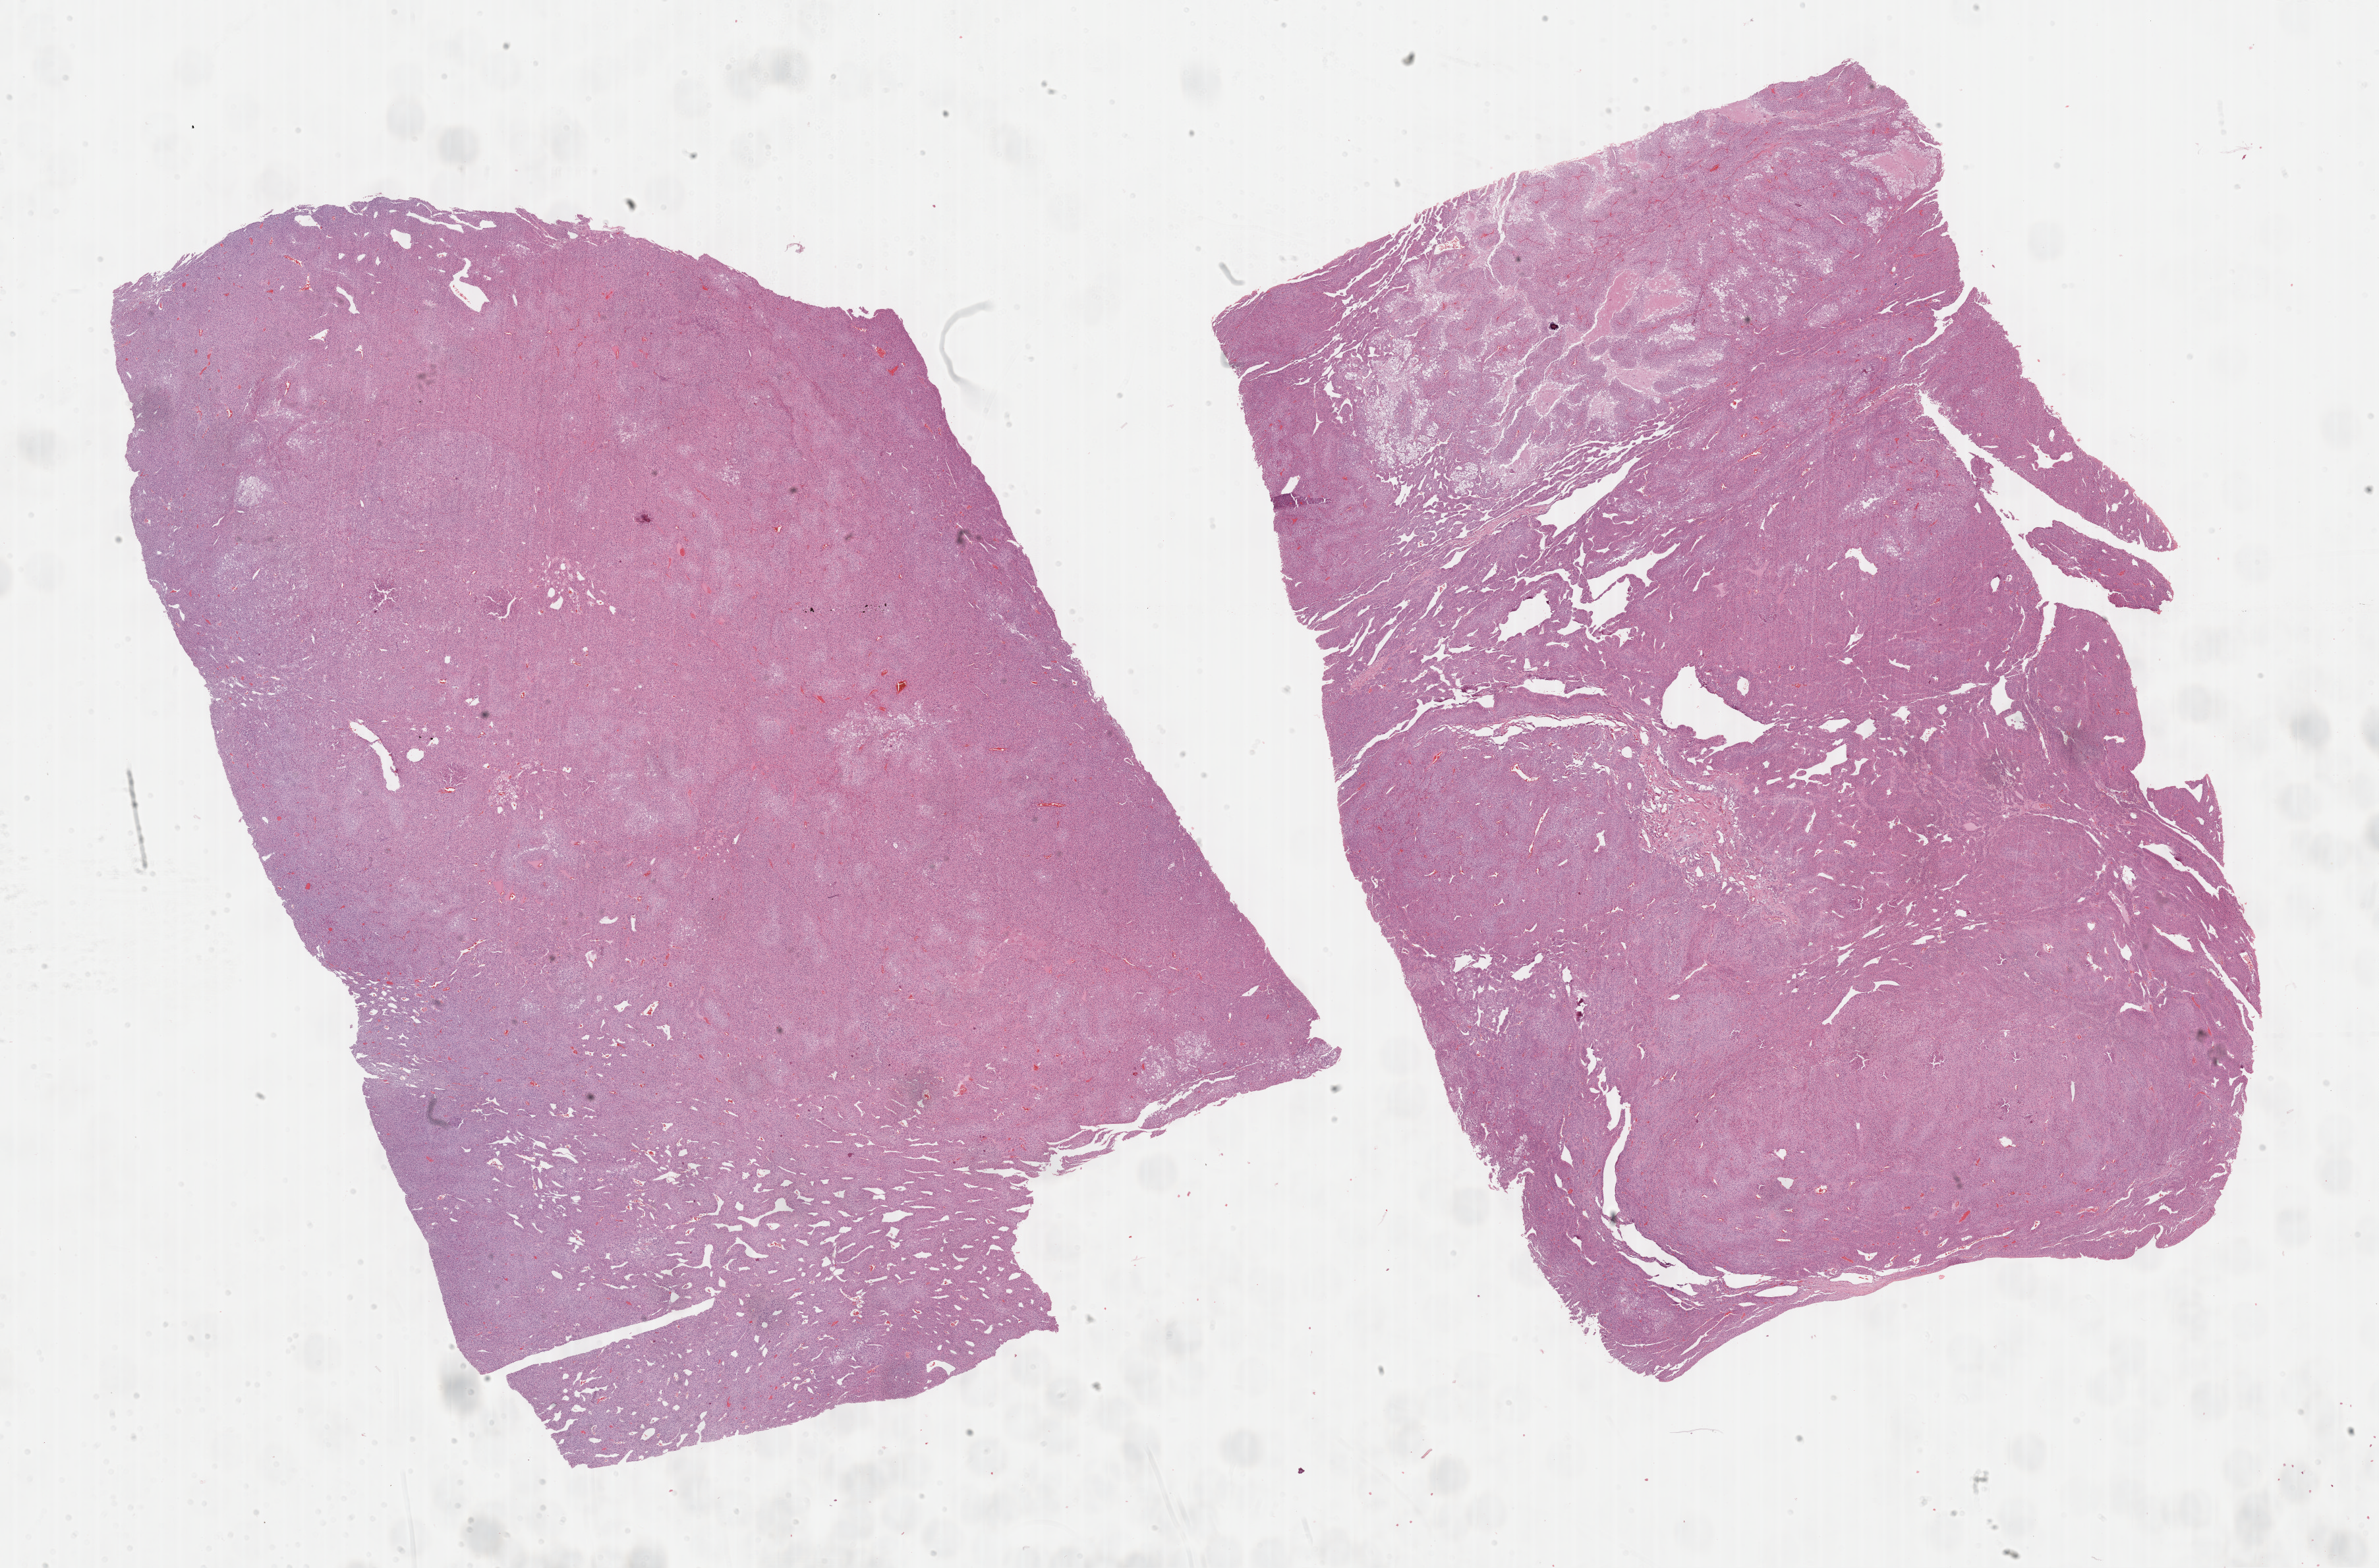
Whole-slide histology image, Hematoxylin and eosin (H&E) stained, whole scanned area (about 29.2 x 19.2 mm, from a 40x scan) shown as a low-resolution overview, formalin-fixed paraffin-embedded (FFPE) diagnostic section, sample: primary tumour, adrenal cortex. Patient: male, age at initial diagnosis 47 years.
Laterality: right. Histologic diagnosis: Adrenal cortical carcinoma.